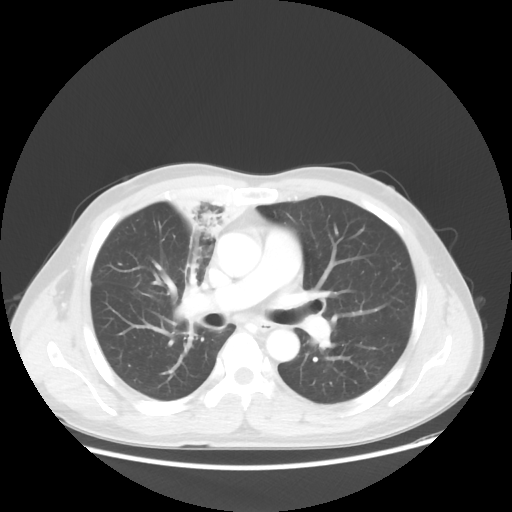
Chest CT, one axial slice. Slice 32 of 56 in the series (ordered by position). Reconstruction kernel STANDARD. 100 kVp. Lung window (W 1500 / L -600 HU). 5 mm slice thickness. 512 × 512 image matrix, field of view 398 × 398 mm. Patient: male, 60 years. From the clinical record (not read from this slice): clinical TNM (as recorded): T2a N1 M0.
Outlined on this slice (bounding box drawn by a radiologist):
- lung tumour (recorded histology: squamous cell carcinoma): bounding box [x1, y1, x2, y2] px = [161, 175, 255, 257]